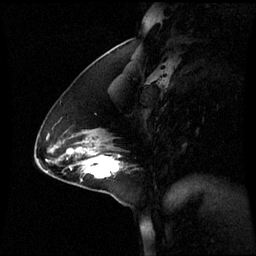
Breast MRI (dynamic contrast-enhanced), one sagittal slice; slice 22 of 60 in the series (ordered by position); dynamic contrast-enhanced series, image 2 of 3 at this slice position (ordered by acquisition); 1.5 T; TE 4.2 ms, TR 8.9 ms; 256 × 256 image matrix, field of view 240 × 240 mm. Female patient, age 44 years. Case-level facts recorded for this patient, not image findings: setting: breast cancer imaged before/during neoadjuvant chemotherapy; receptor status: triple-negative.
Outlined on this slice (semi-automatic segmentation, software-assisted and operator-edited):
- analysis volume of interest (the breast-tissue region the enhancement analysis was run in; not a lesion): bounding box <76,150,128,181> (left, top, right, bottom; pixels)
- tumour enhancement mask (voxels above the 70 % enhancement threshold inside the analysis volume of interest): <82,156,120,179>